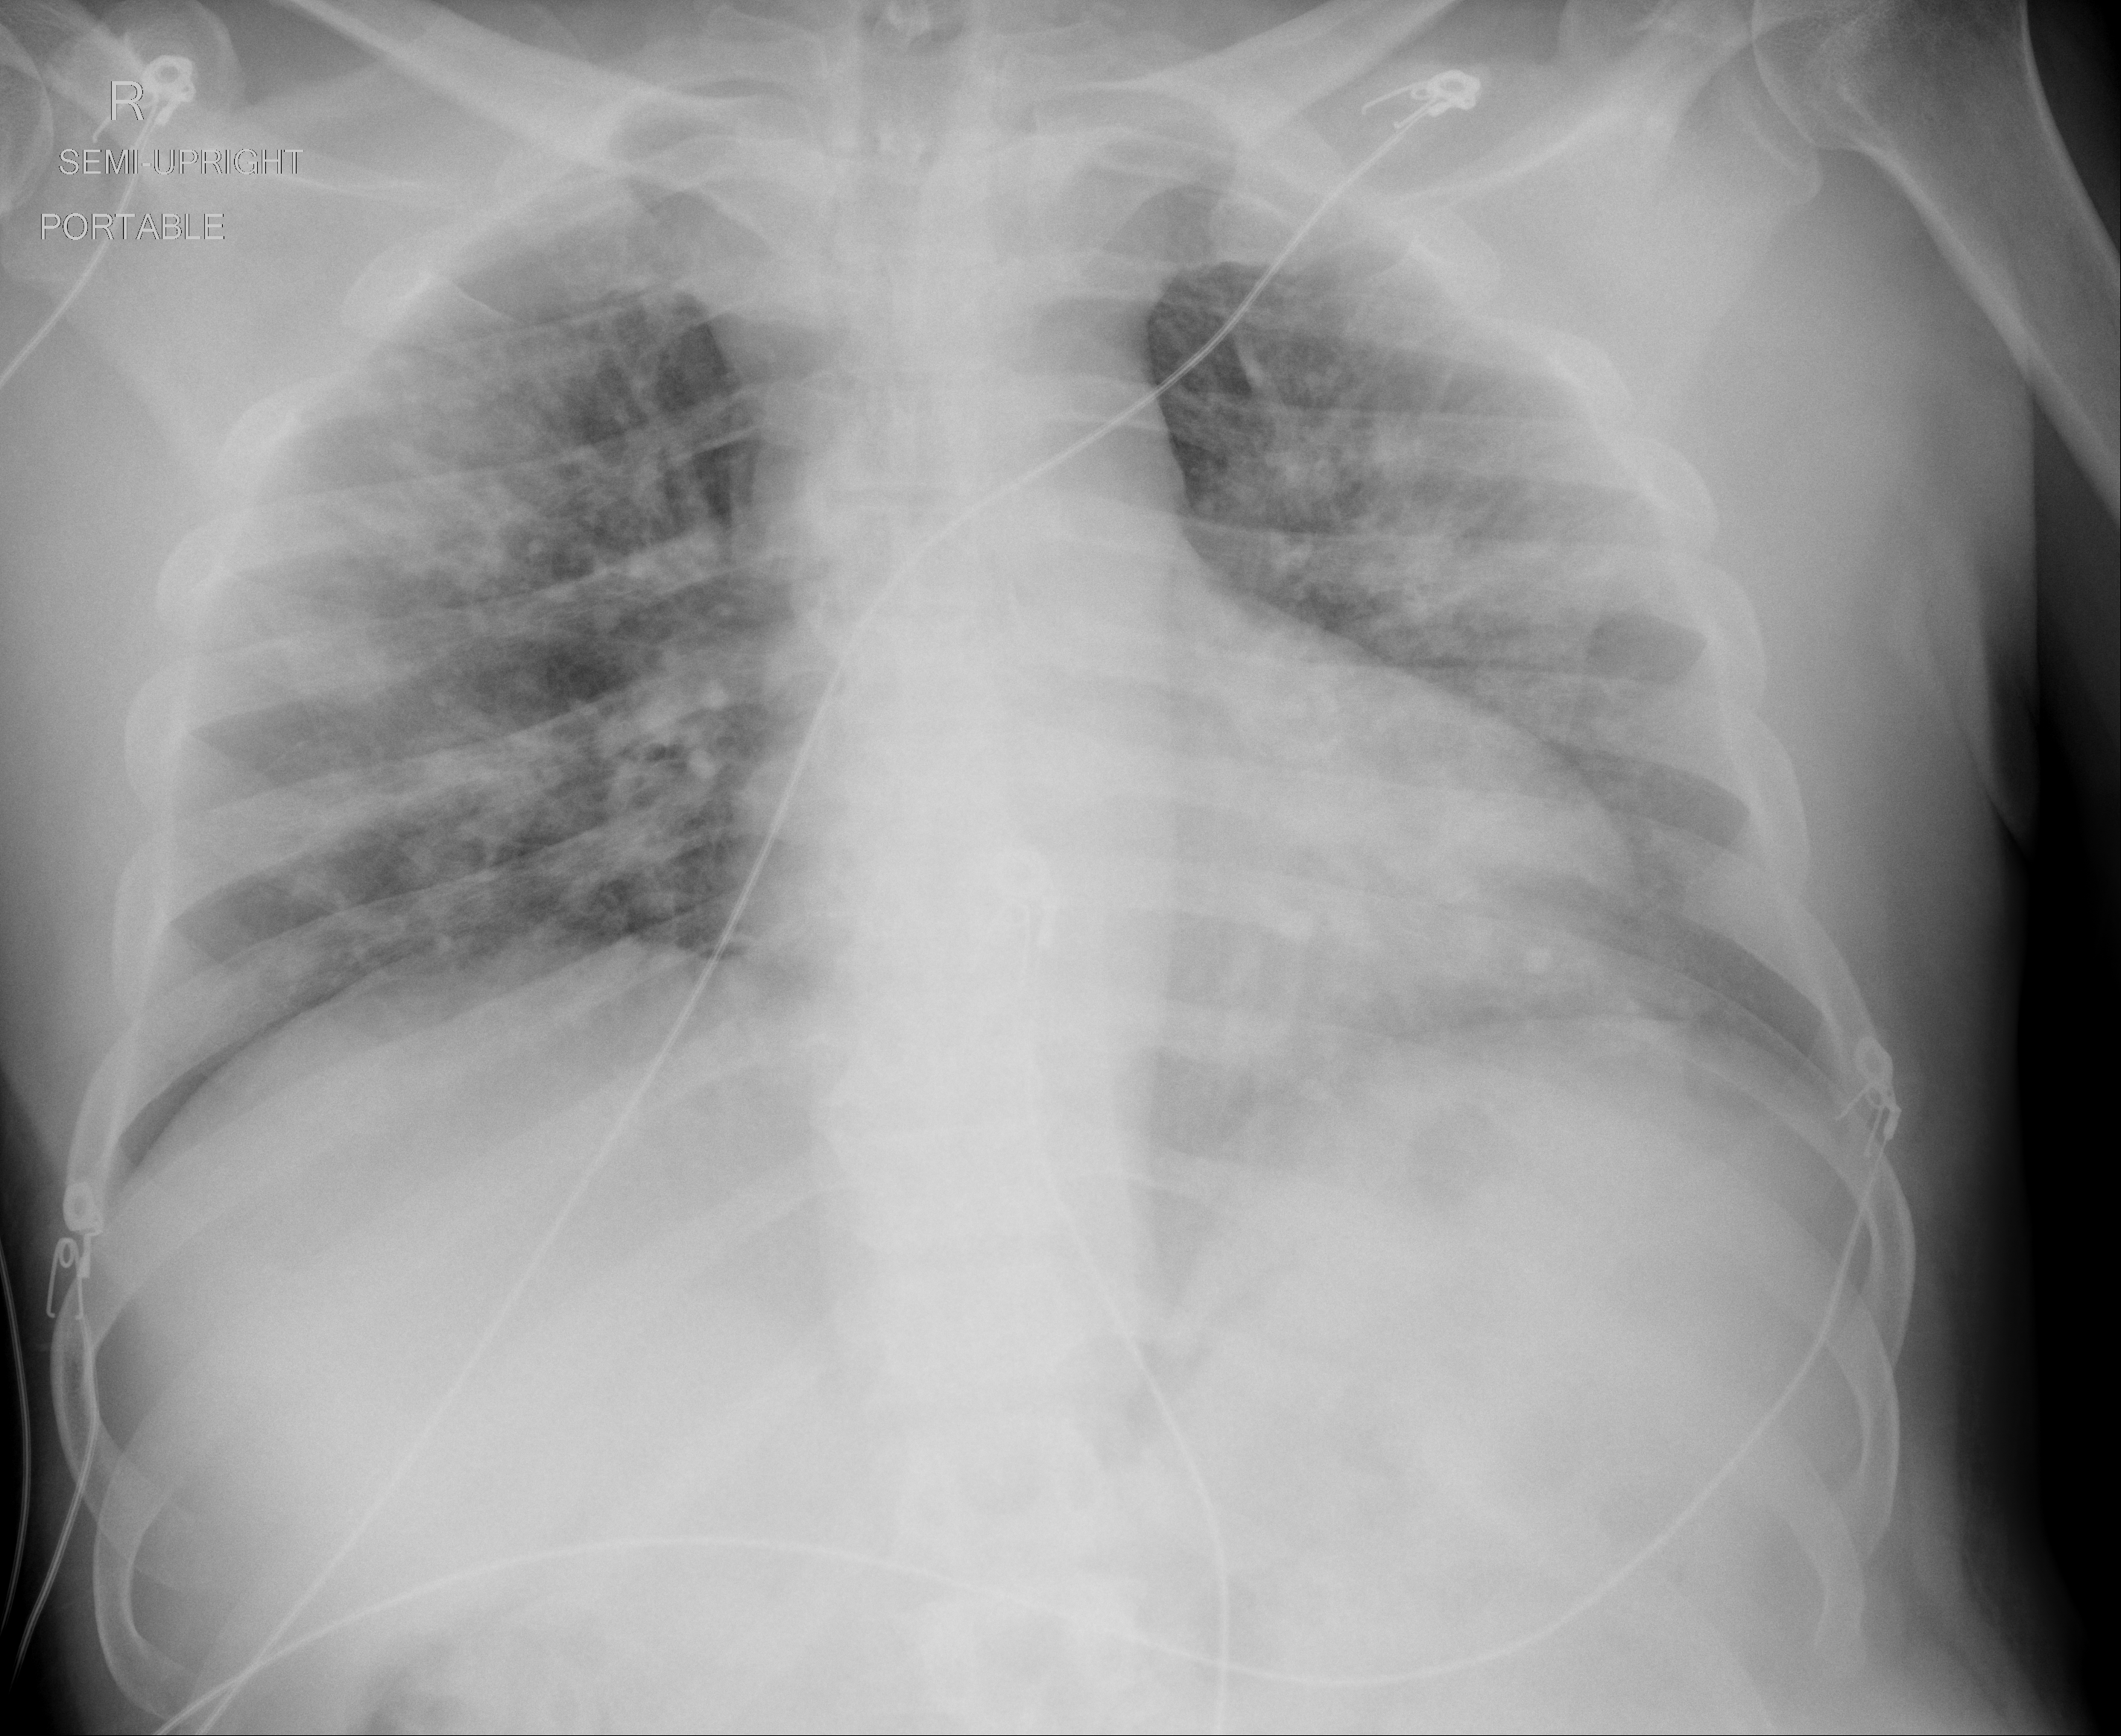
Chest X-ray, AP projection. Male patient, age 55 years; imaged 2 days after the COVID-19 diagnosis.
Key findings recorded by the radiologist: Peripheral patchy opacities with a mid lung predominance in the bilateral lungs.